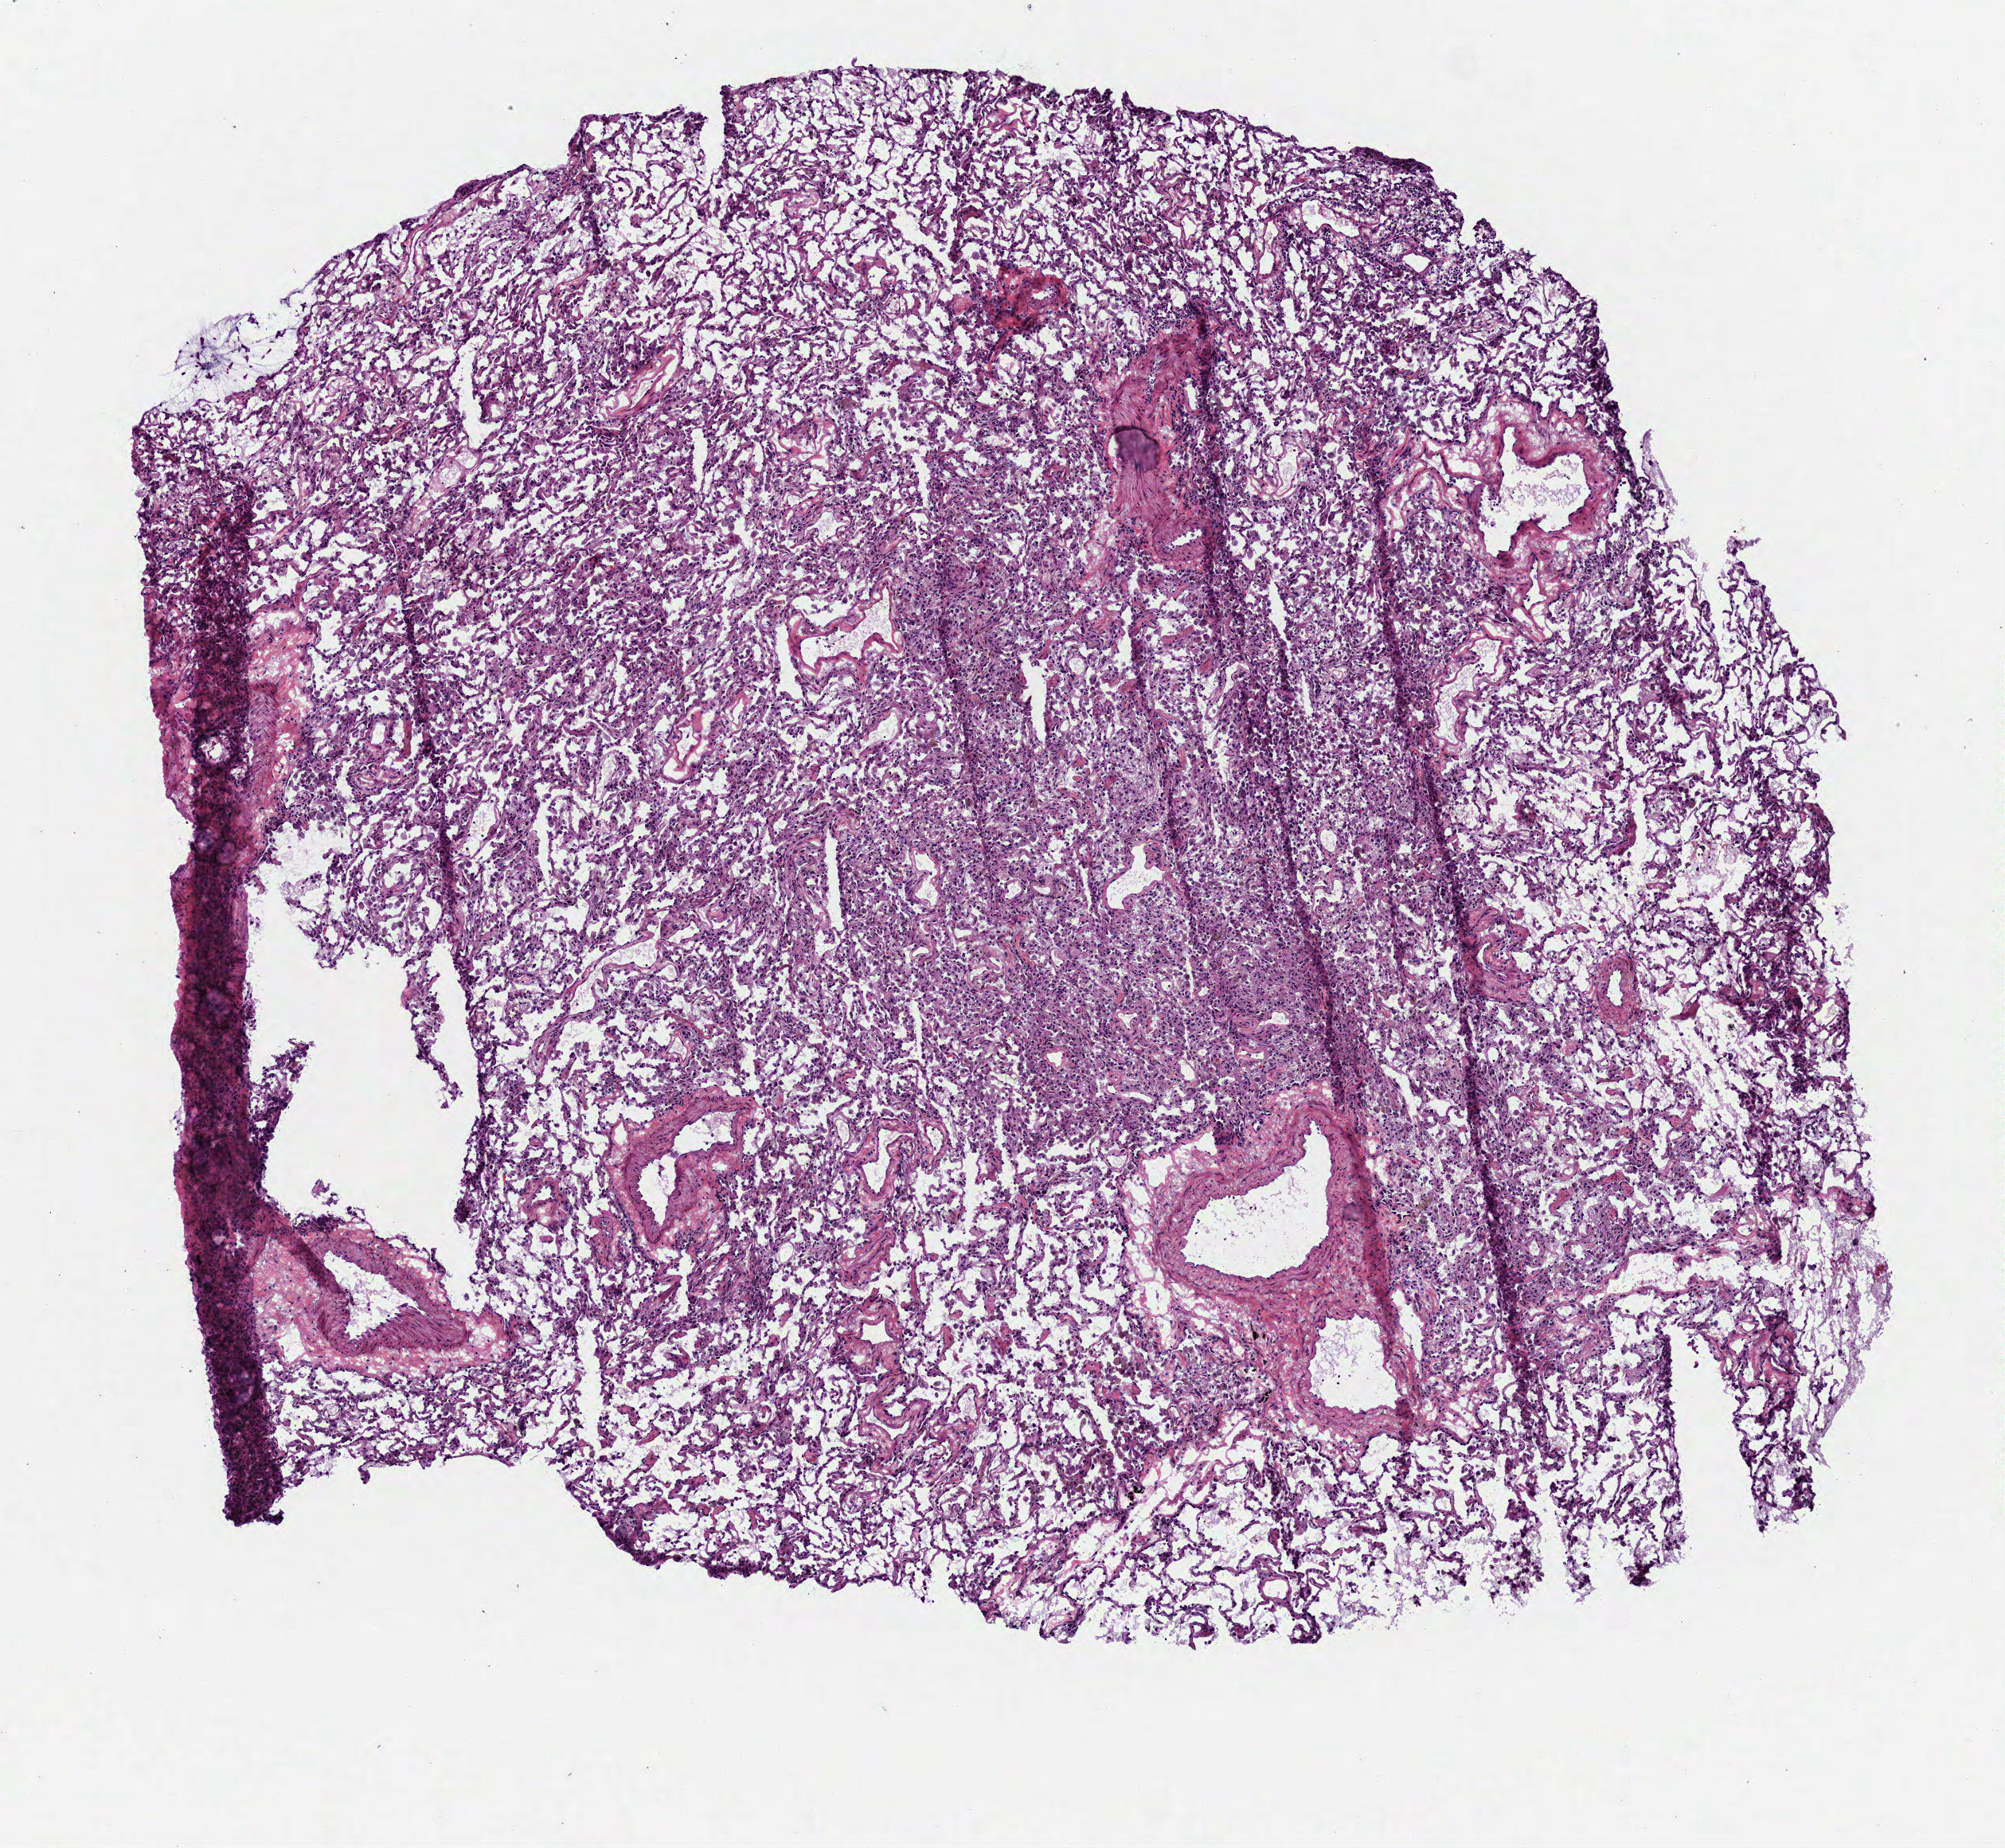
Whole-slide histology image, Hematoxylin and eosin (H&E) stained — shown as a low-resolution overview of the whole scanned area (about 5.1 x 4.7 mm, slide scanned at 40x), frozen section, solid tissue normal (non-tumour tissue) sample from the lung. Male patient; age at initial diagnosis 66 years.
This section: solid tissue normal (non-tumour) sample from the same patient. Patient diagnosis: Squamous cell carcinoma, NOS (lower lobe, lung).